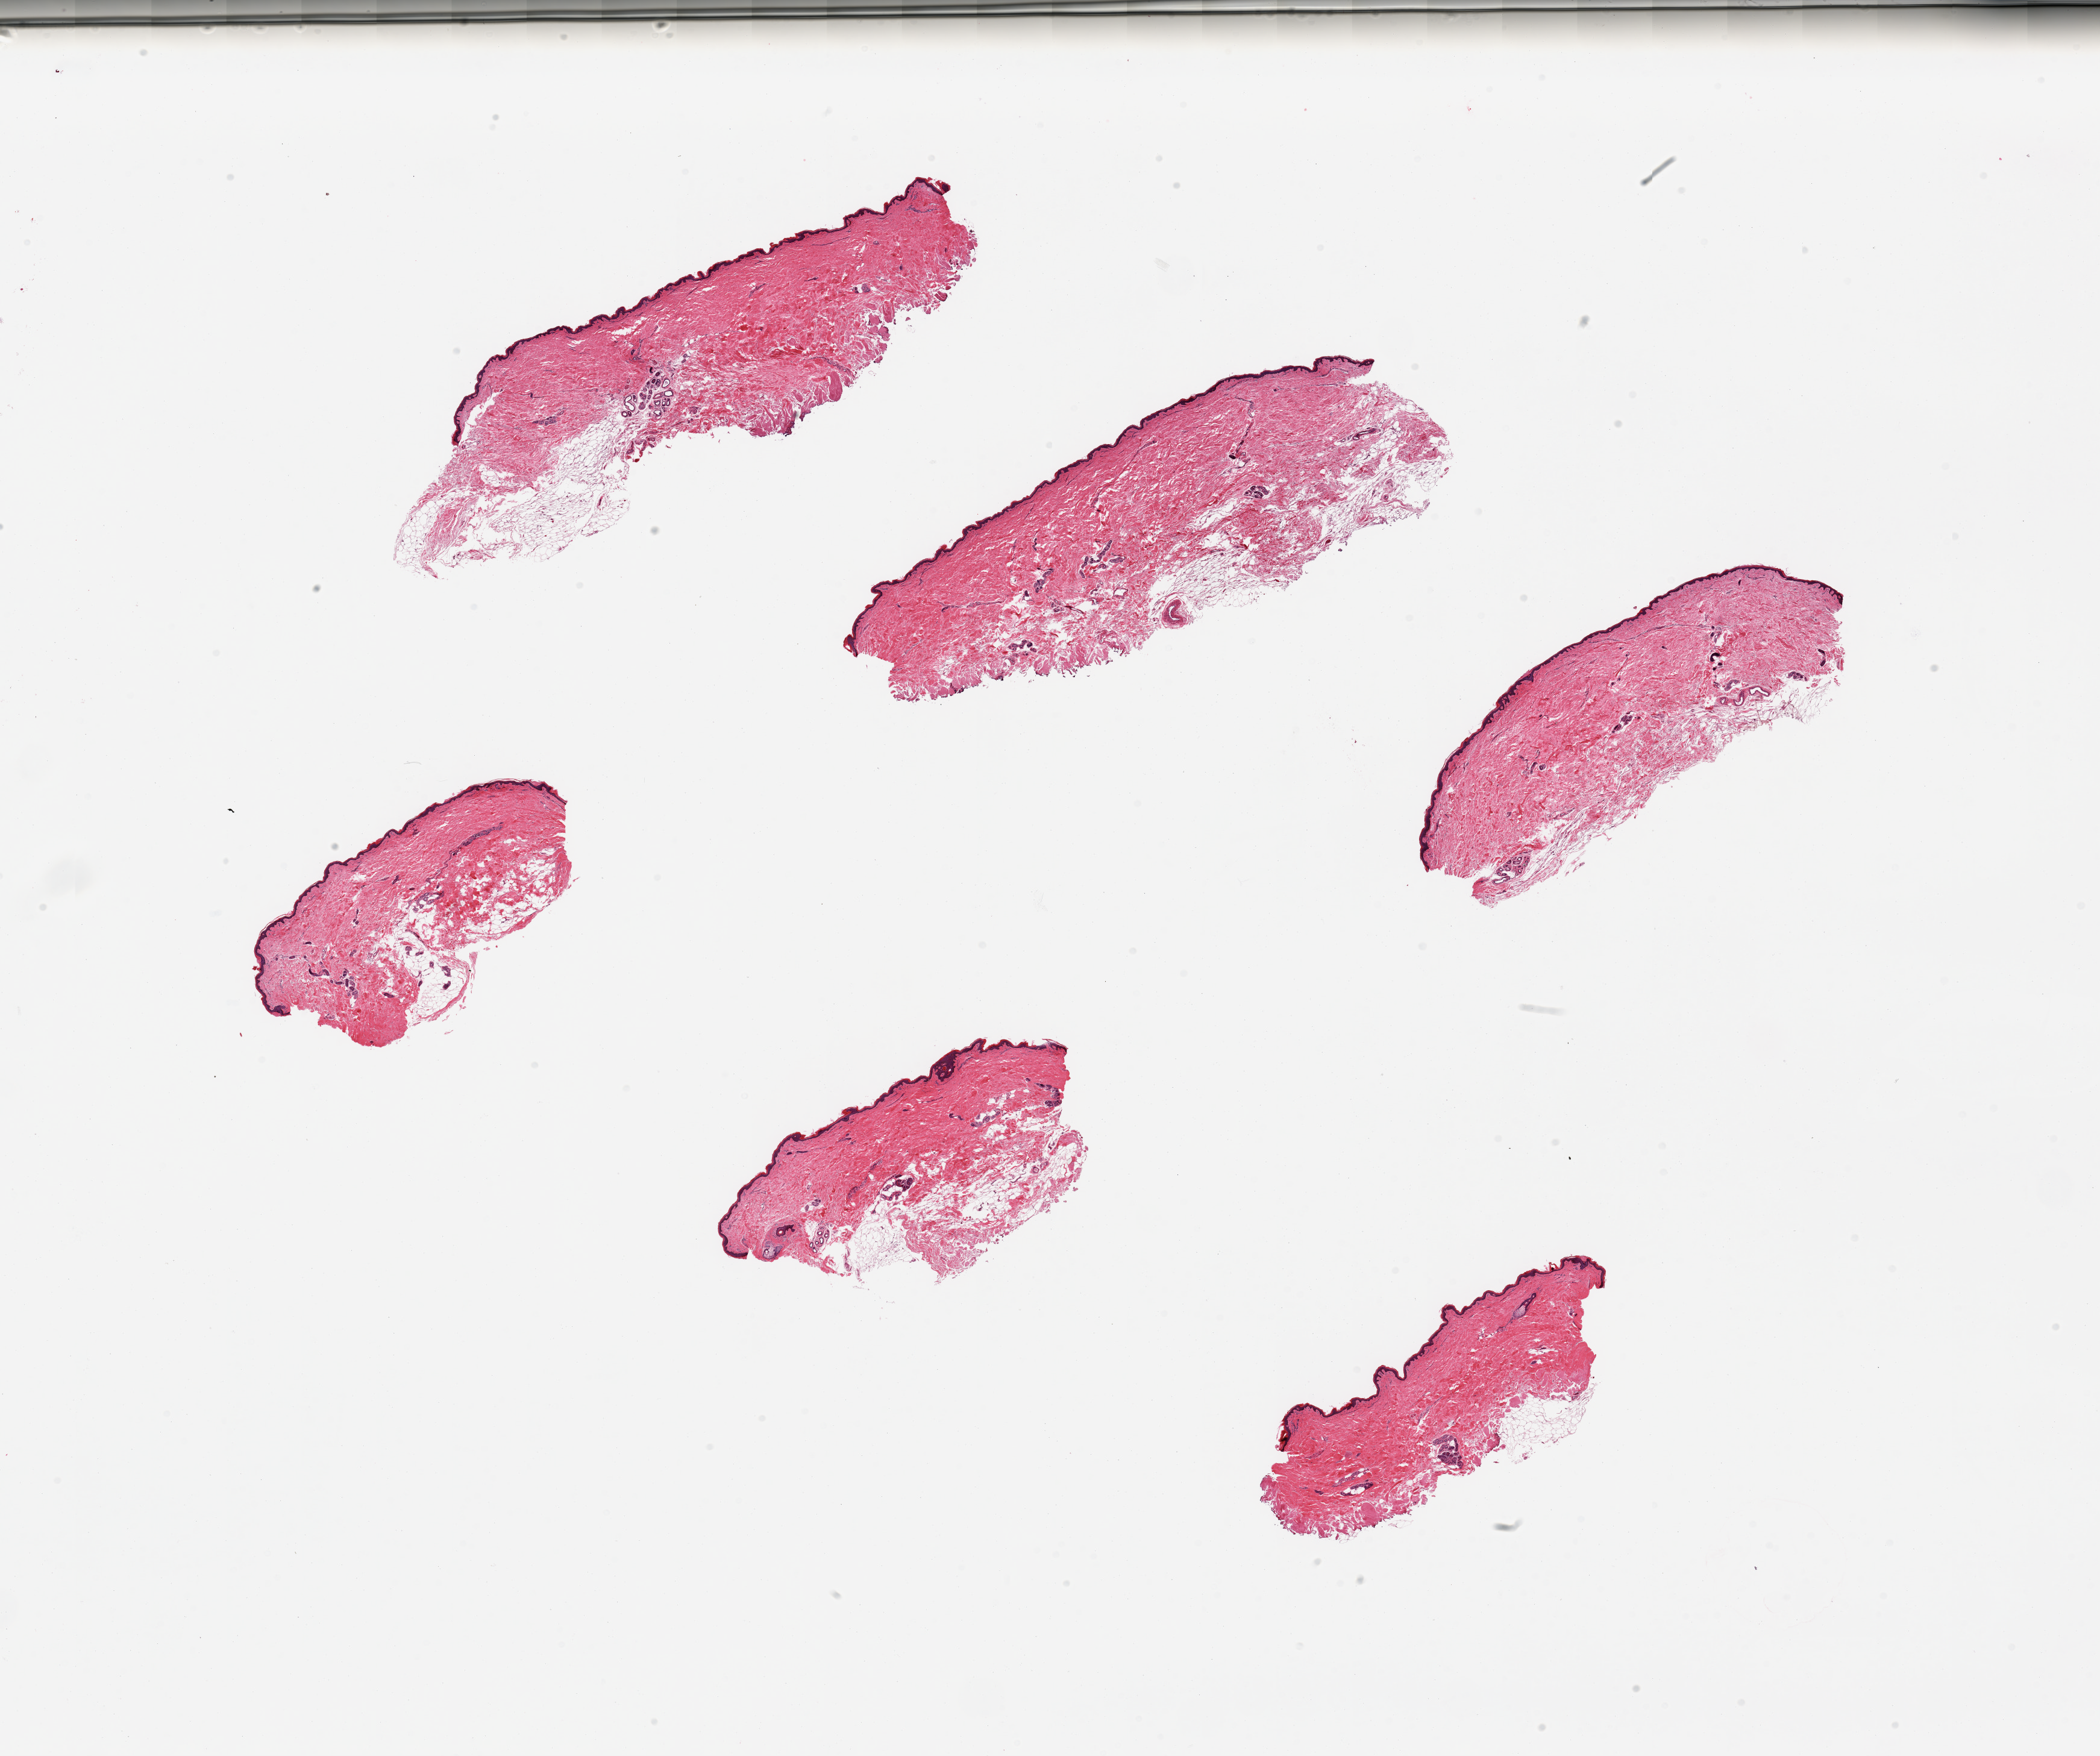
Digitized H&E-stained section — a low-resolution overview of the entire scanned area, about 27.6 x 23.0 mm. PAXgene-fixed paraffin-embedded (PFPE) section. Section of skin of suprapubic region (target tissue). Tissue donor sample.
Pathologist's review note for this sample: 6 pieces; up to 1 mm subcutaneous fat.